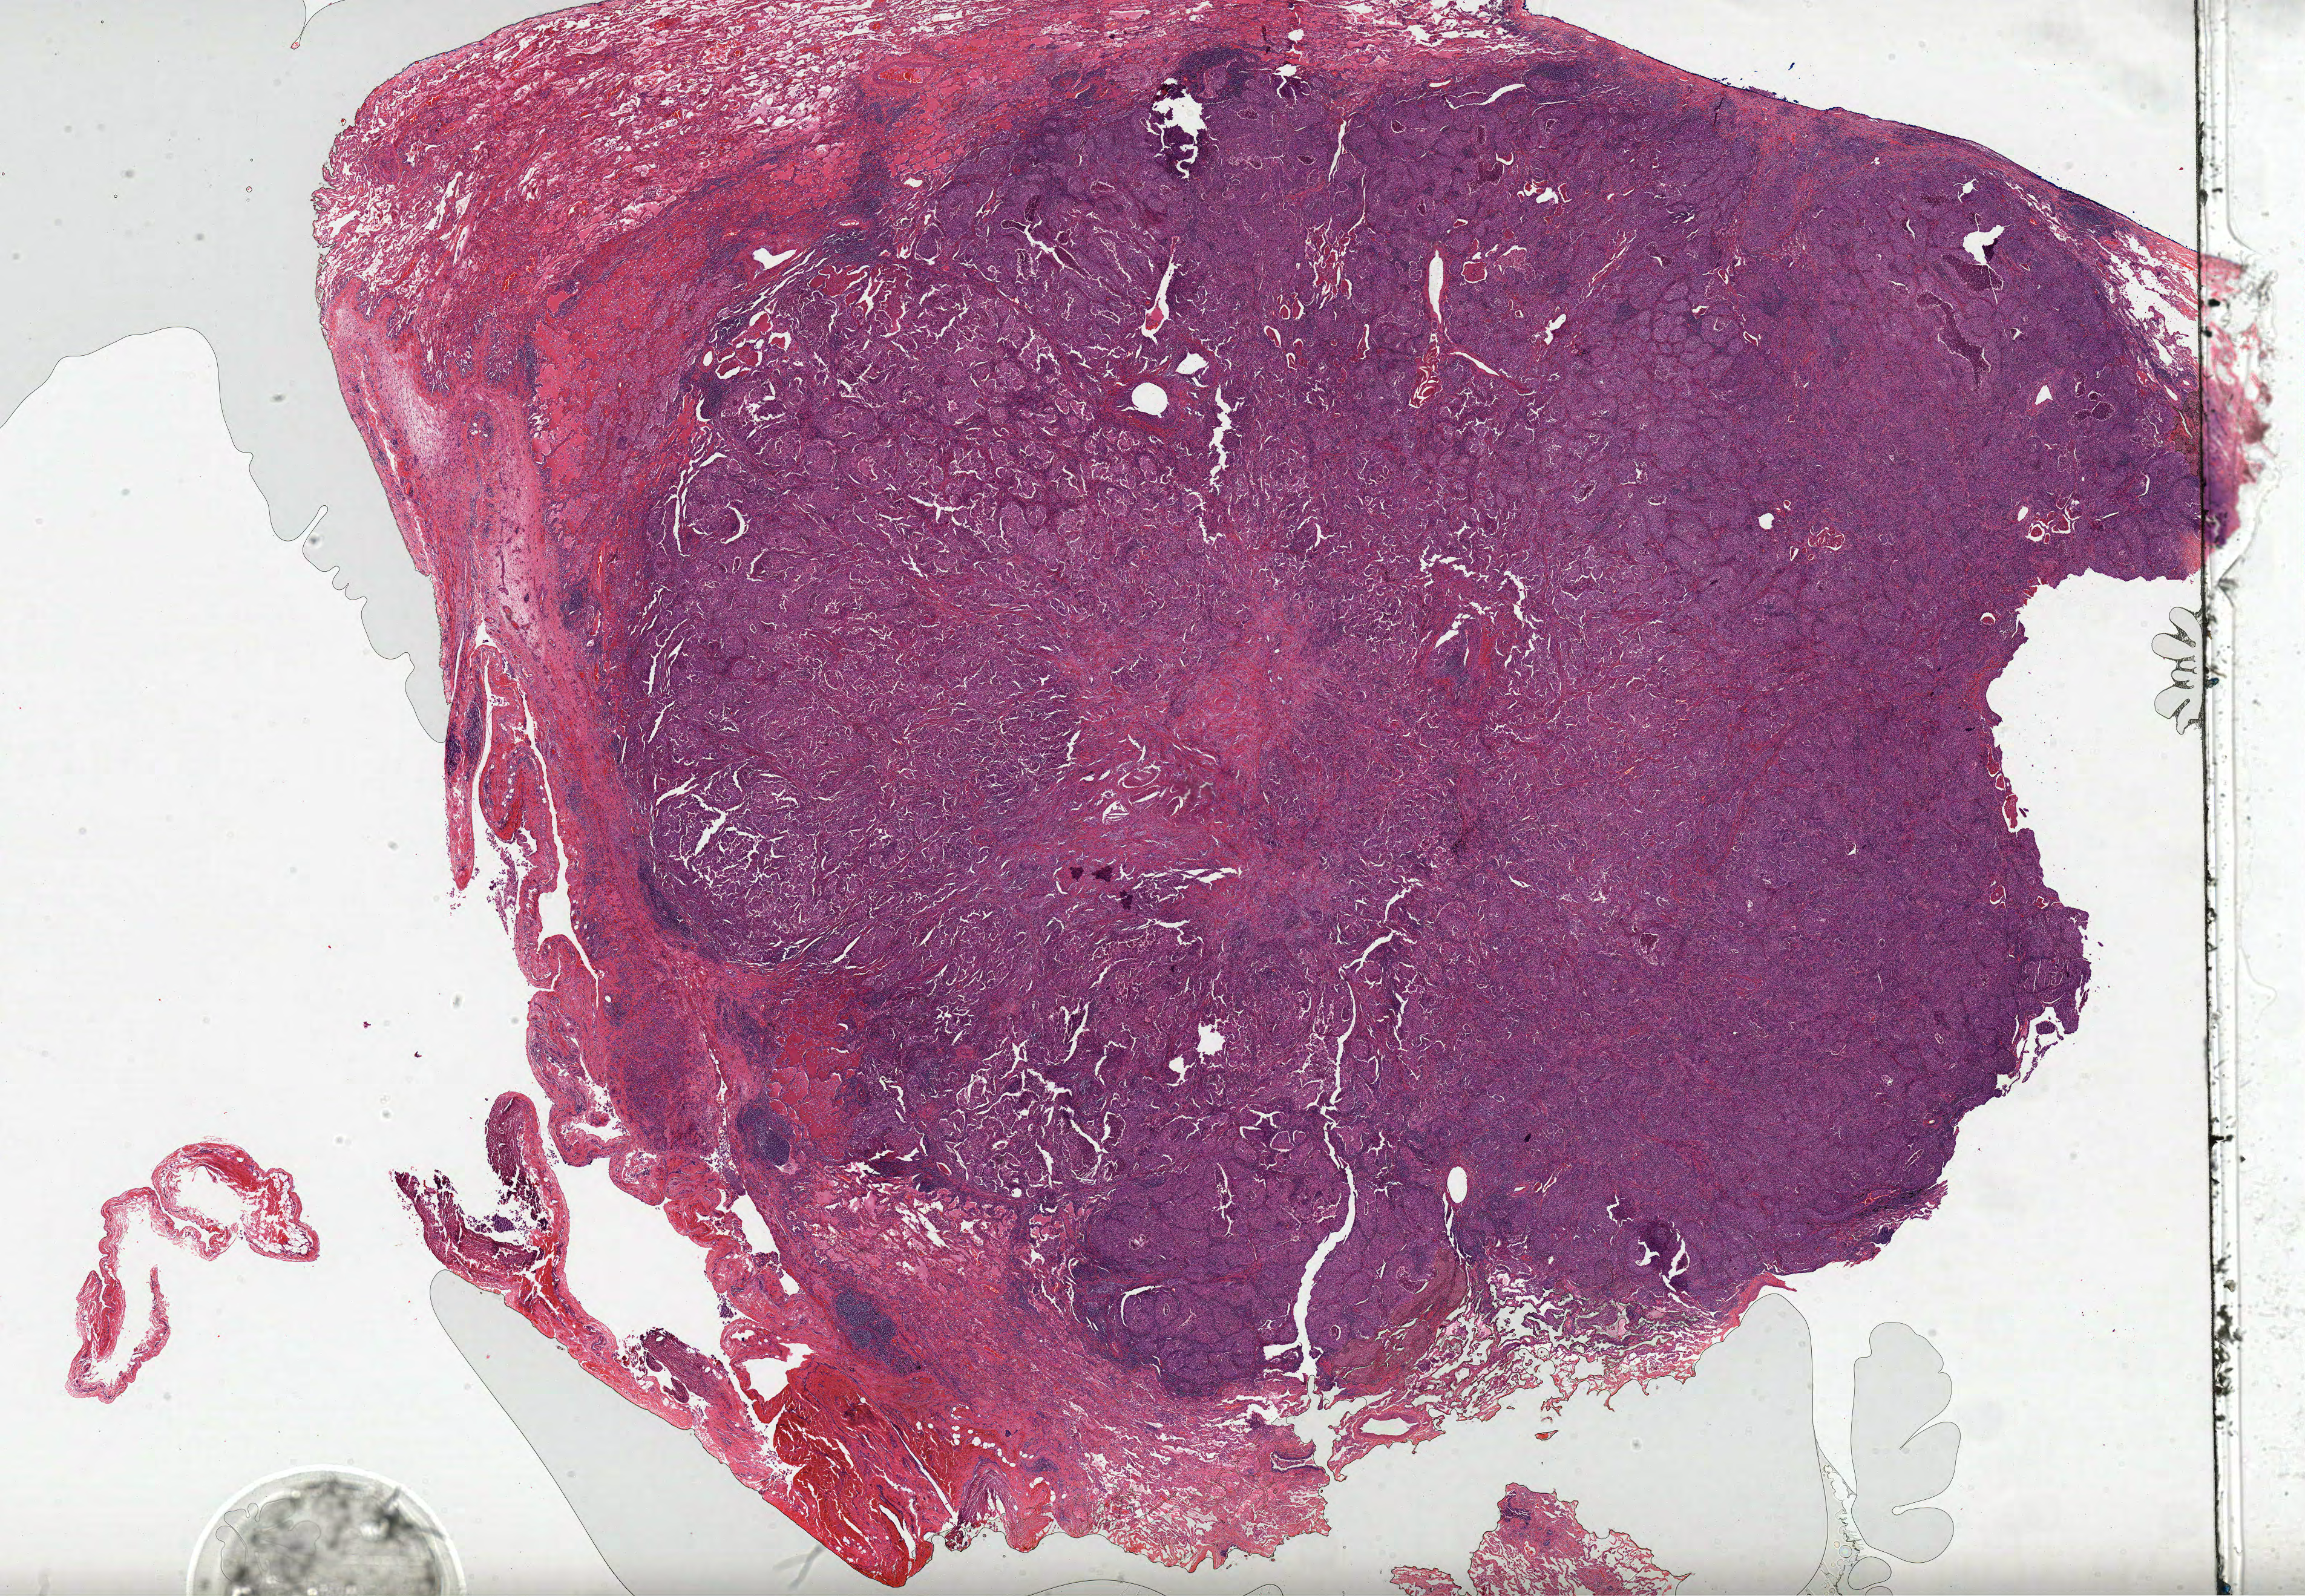
Hematoxylin and eosin (H&E) stained whole-slide image, shown as a low-resolution overview of the whole scanned area (about 30.7 x 21.3 mm, slide scanned at 20x), formalin-fixed paraffin-embedded (FFPE) diagnostic section, sample: primary tumour, lung. Female patient; age at initial diagnosis 70 years.
* laterality: right
* AJCC pathologic stage: IA (6th edition)
* histologic diagnosis: Squamous cell carcinoma, NOS